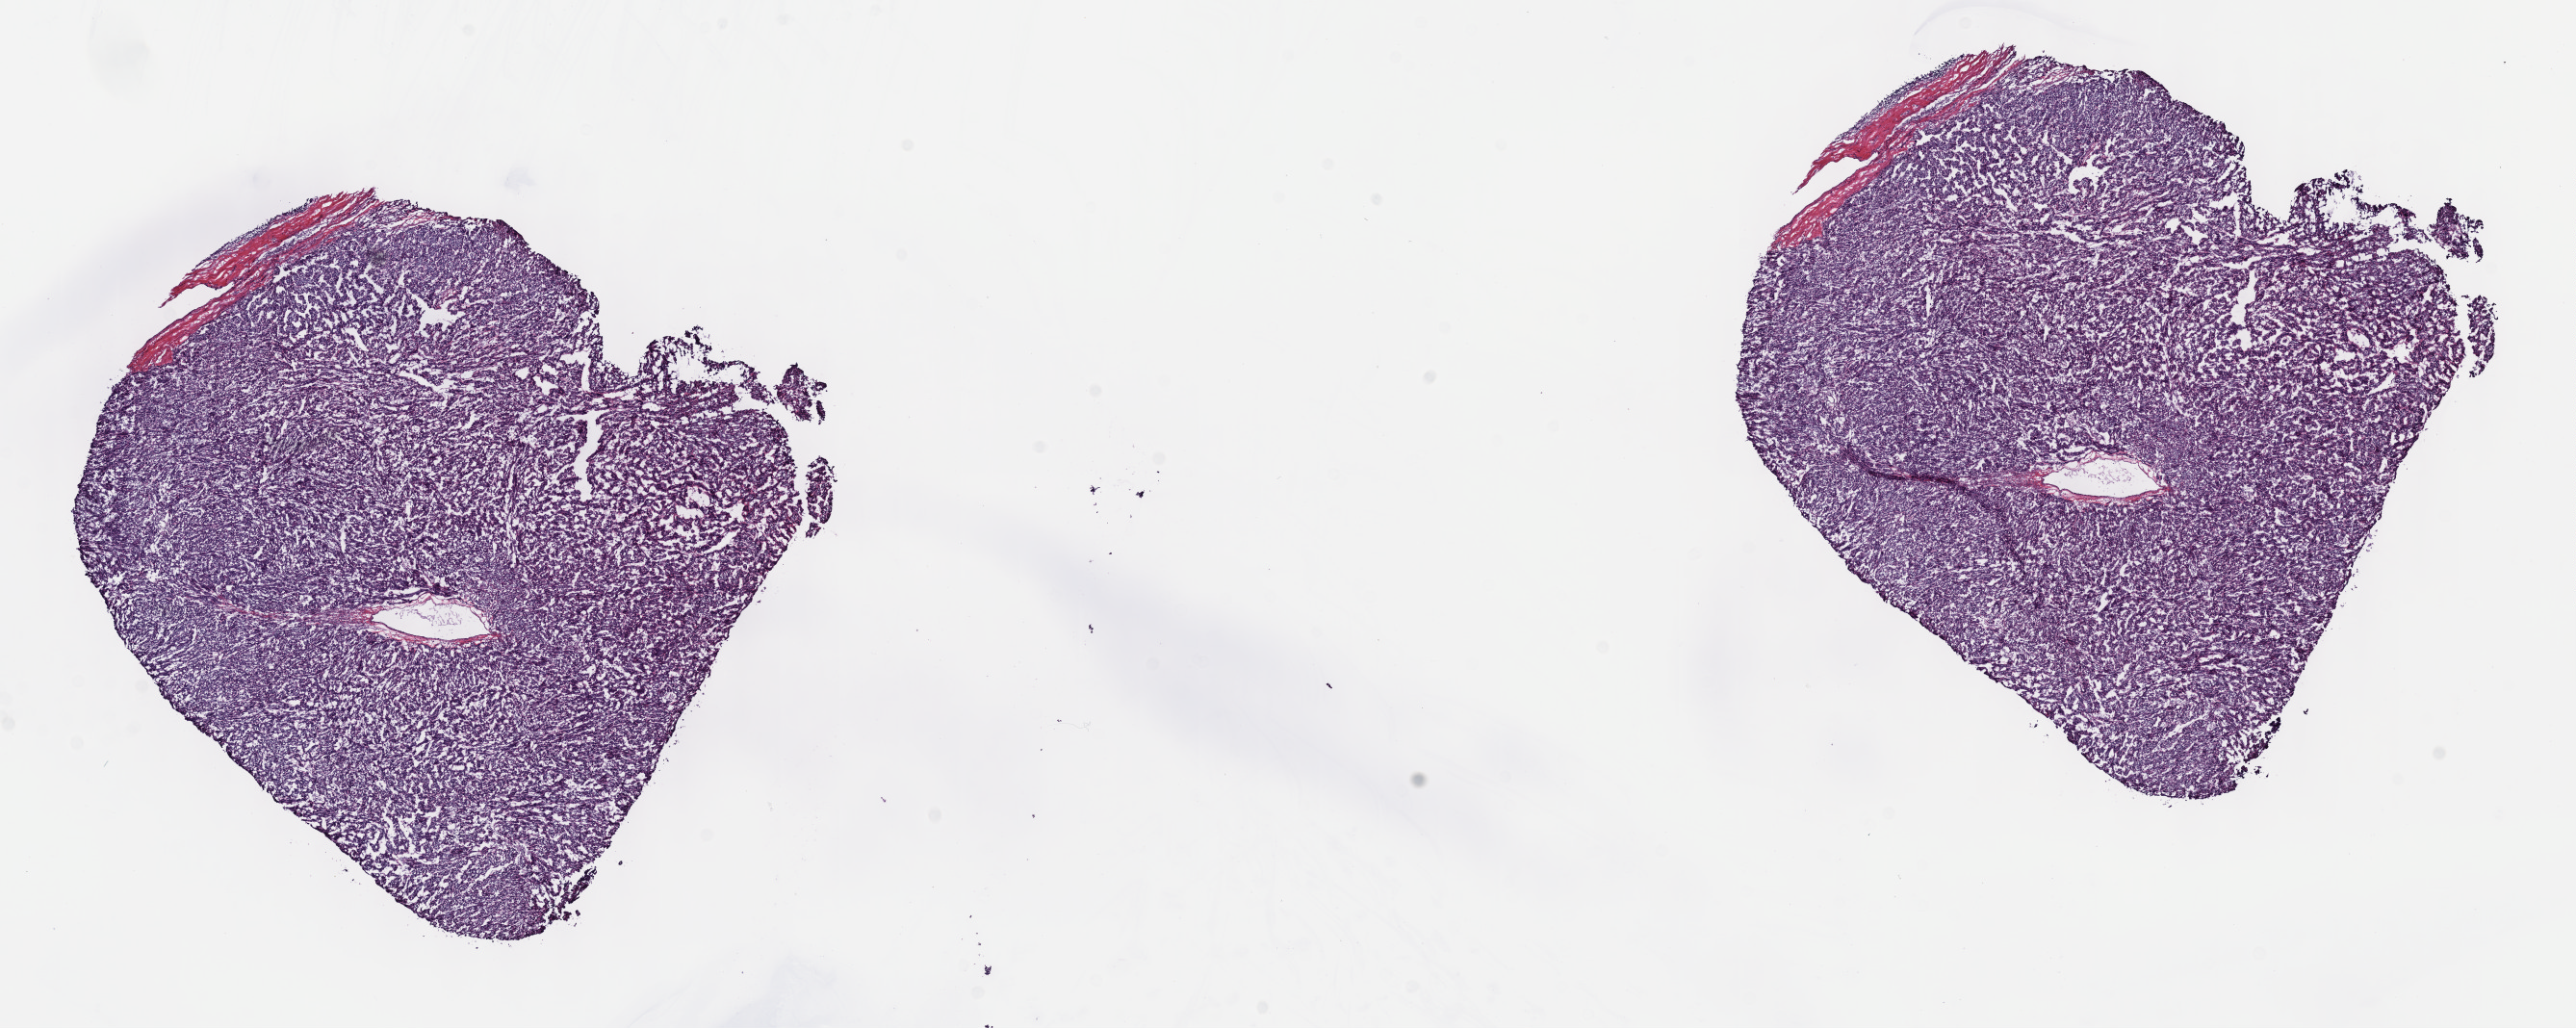
Digitized H&E tissue section (whole slide), shown as a low-resolution overview of the whole scanned area (about 21.6 x 8.6 mm, acquisition: 40x scan), frozen section from the top of the tissue portion, thymus, primary tumour sample. Male patient; age at initial diagnosis 50 years. Composition of this section per pathologist review: tumour cells 98%, tumour nuclei 80%, normal cells 0%, stromal cells 2%, necrosis 0%. Infiltration values recorded for this section: lymphocyte infiltration 2%, monocyte infiltration 0%, neutrophil infiltration 0%.
Histologic diagnosis: Thymoma, type A, malignant.